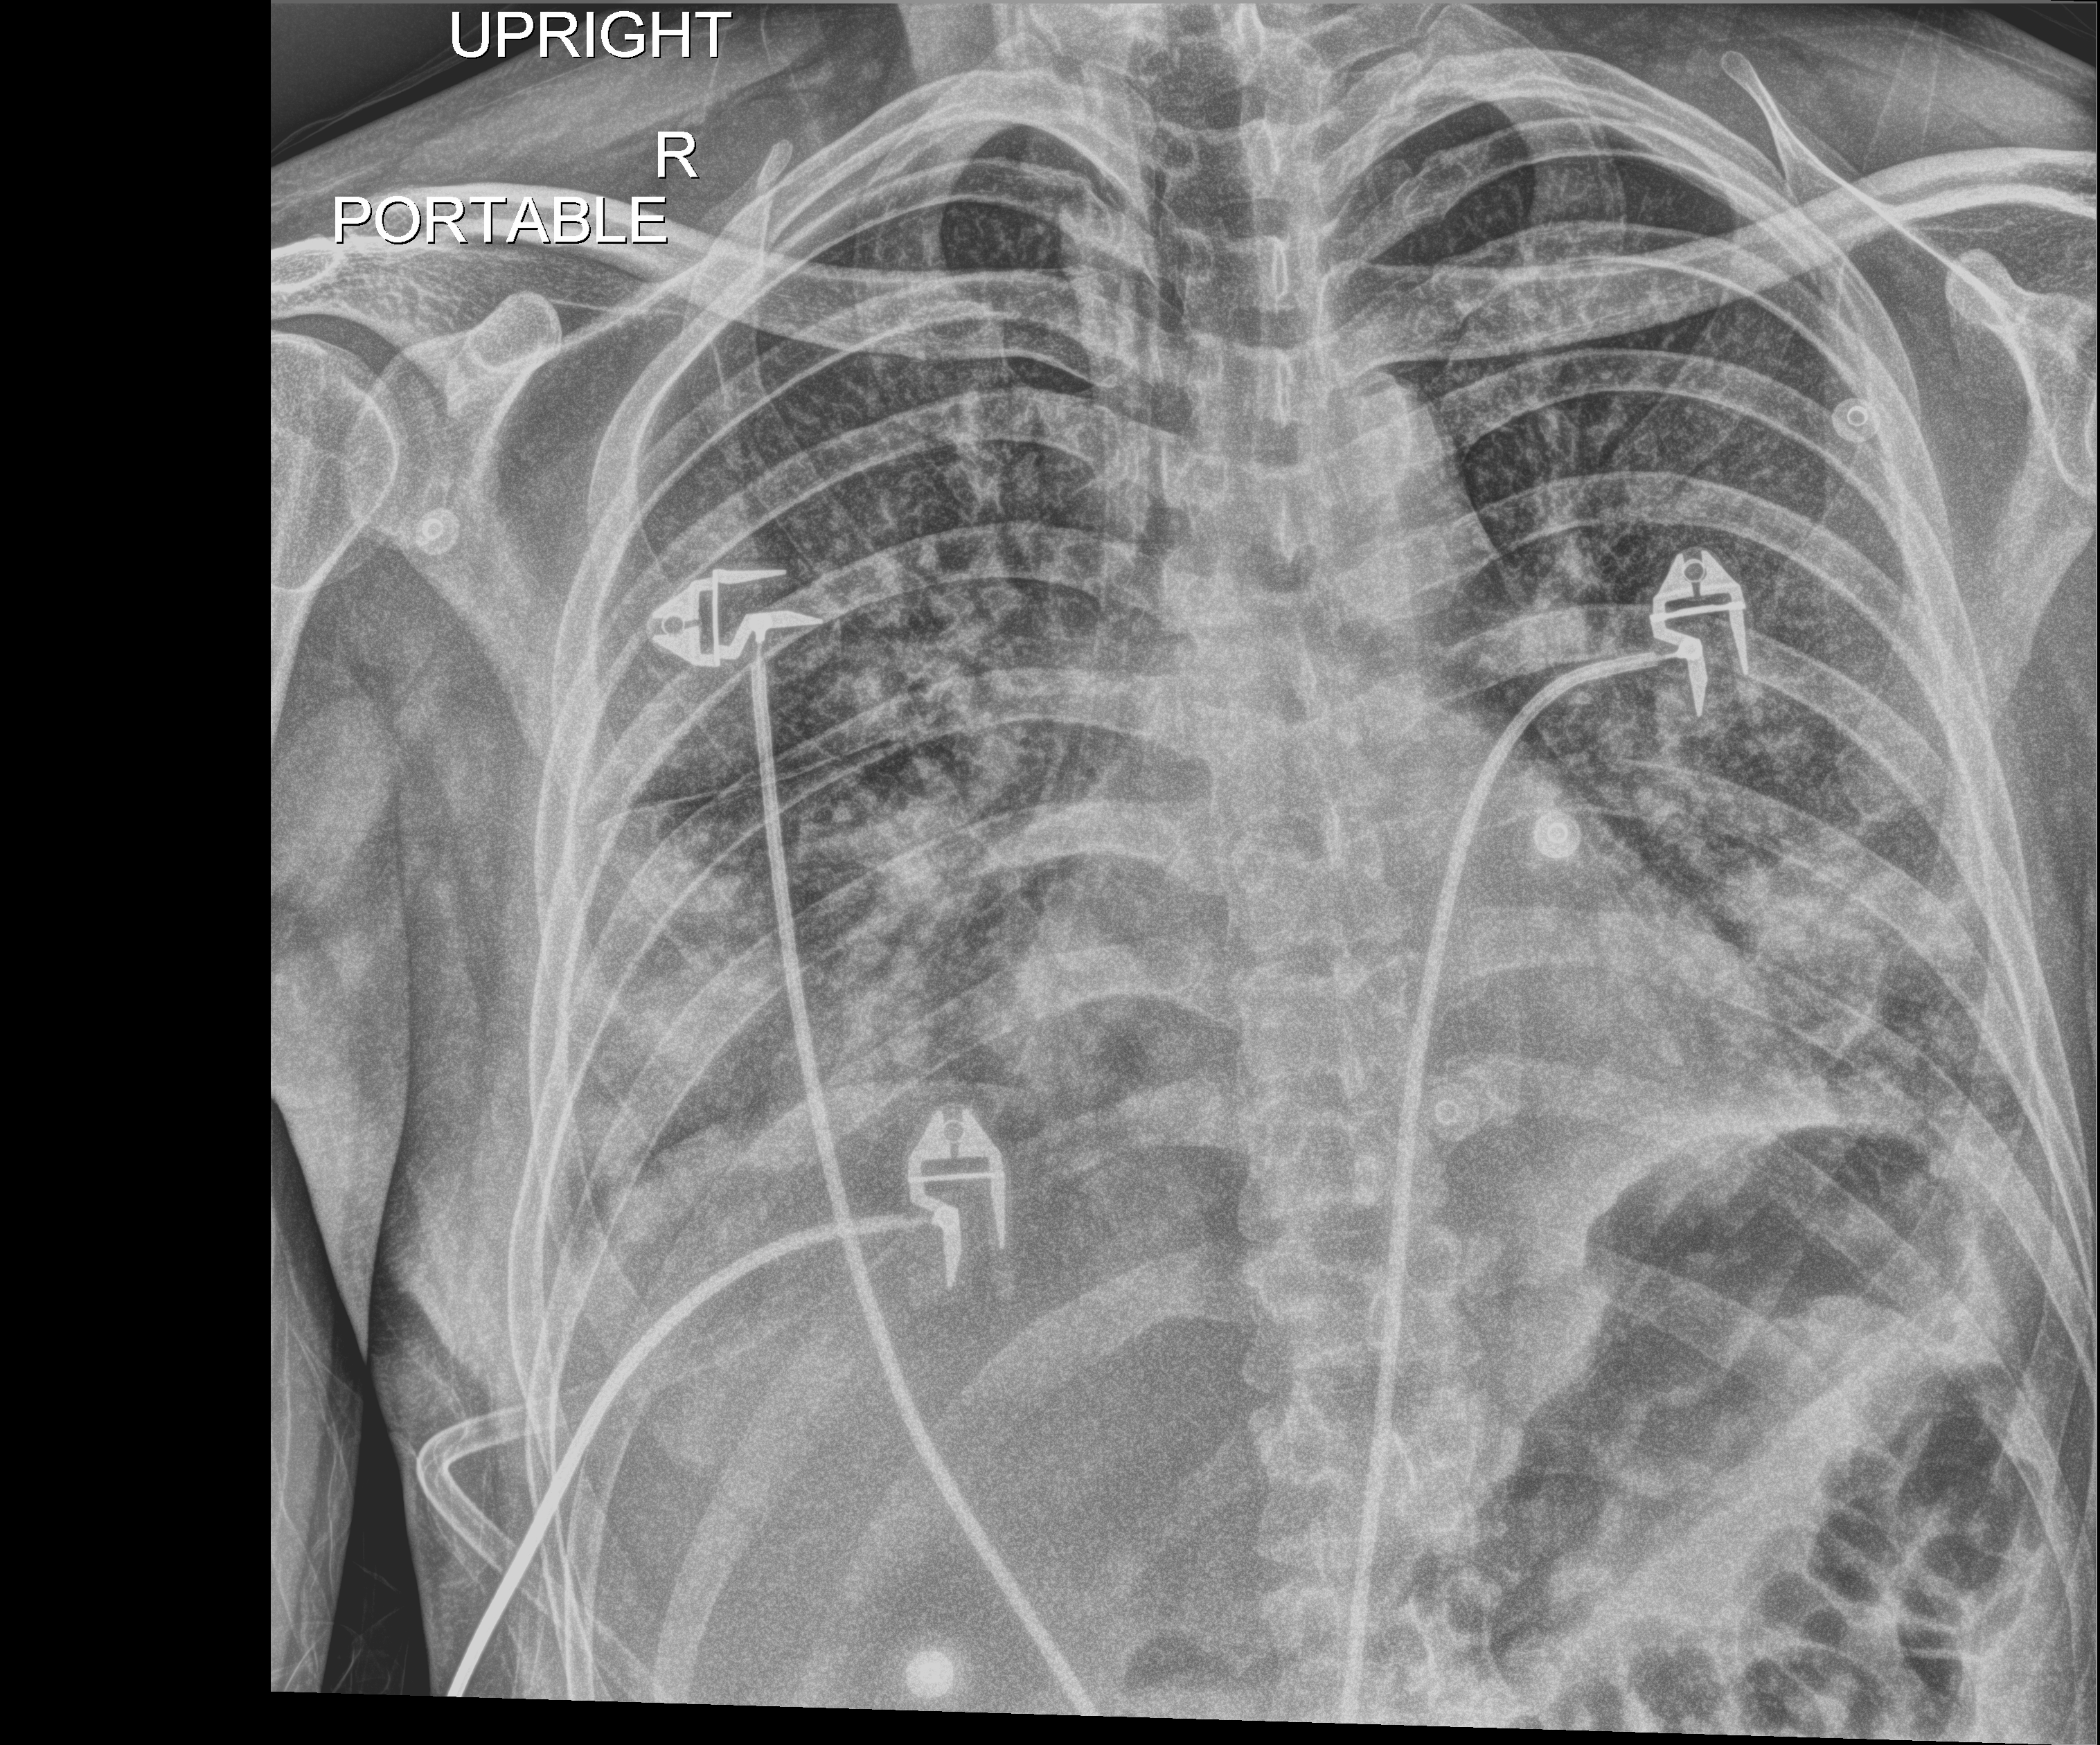
Chest X-ray (portable); anteroposterior (AP) projection. Patient hospitalised with COVID-19; male, aged 18–59 years.
Admission-level facts for this patient (not findings on this image; timing relative to this image not recorded): mechanically ventilated during this hospital stay: no; admitted to intensive care during this hospital stay: no; smoking status (admission record): never.